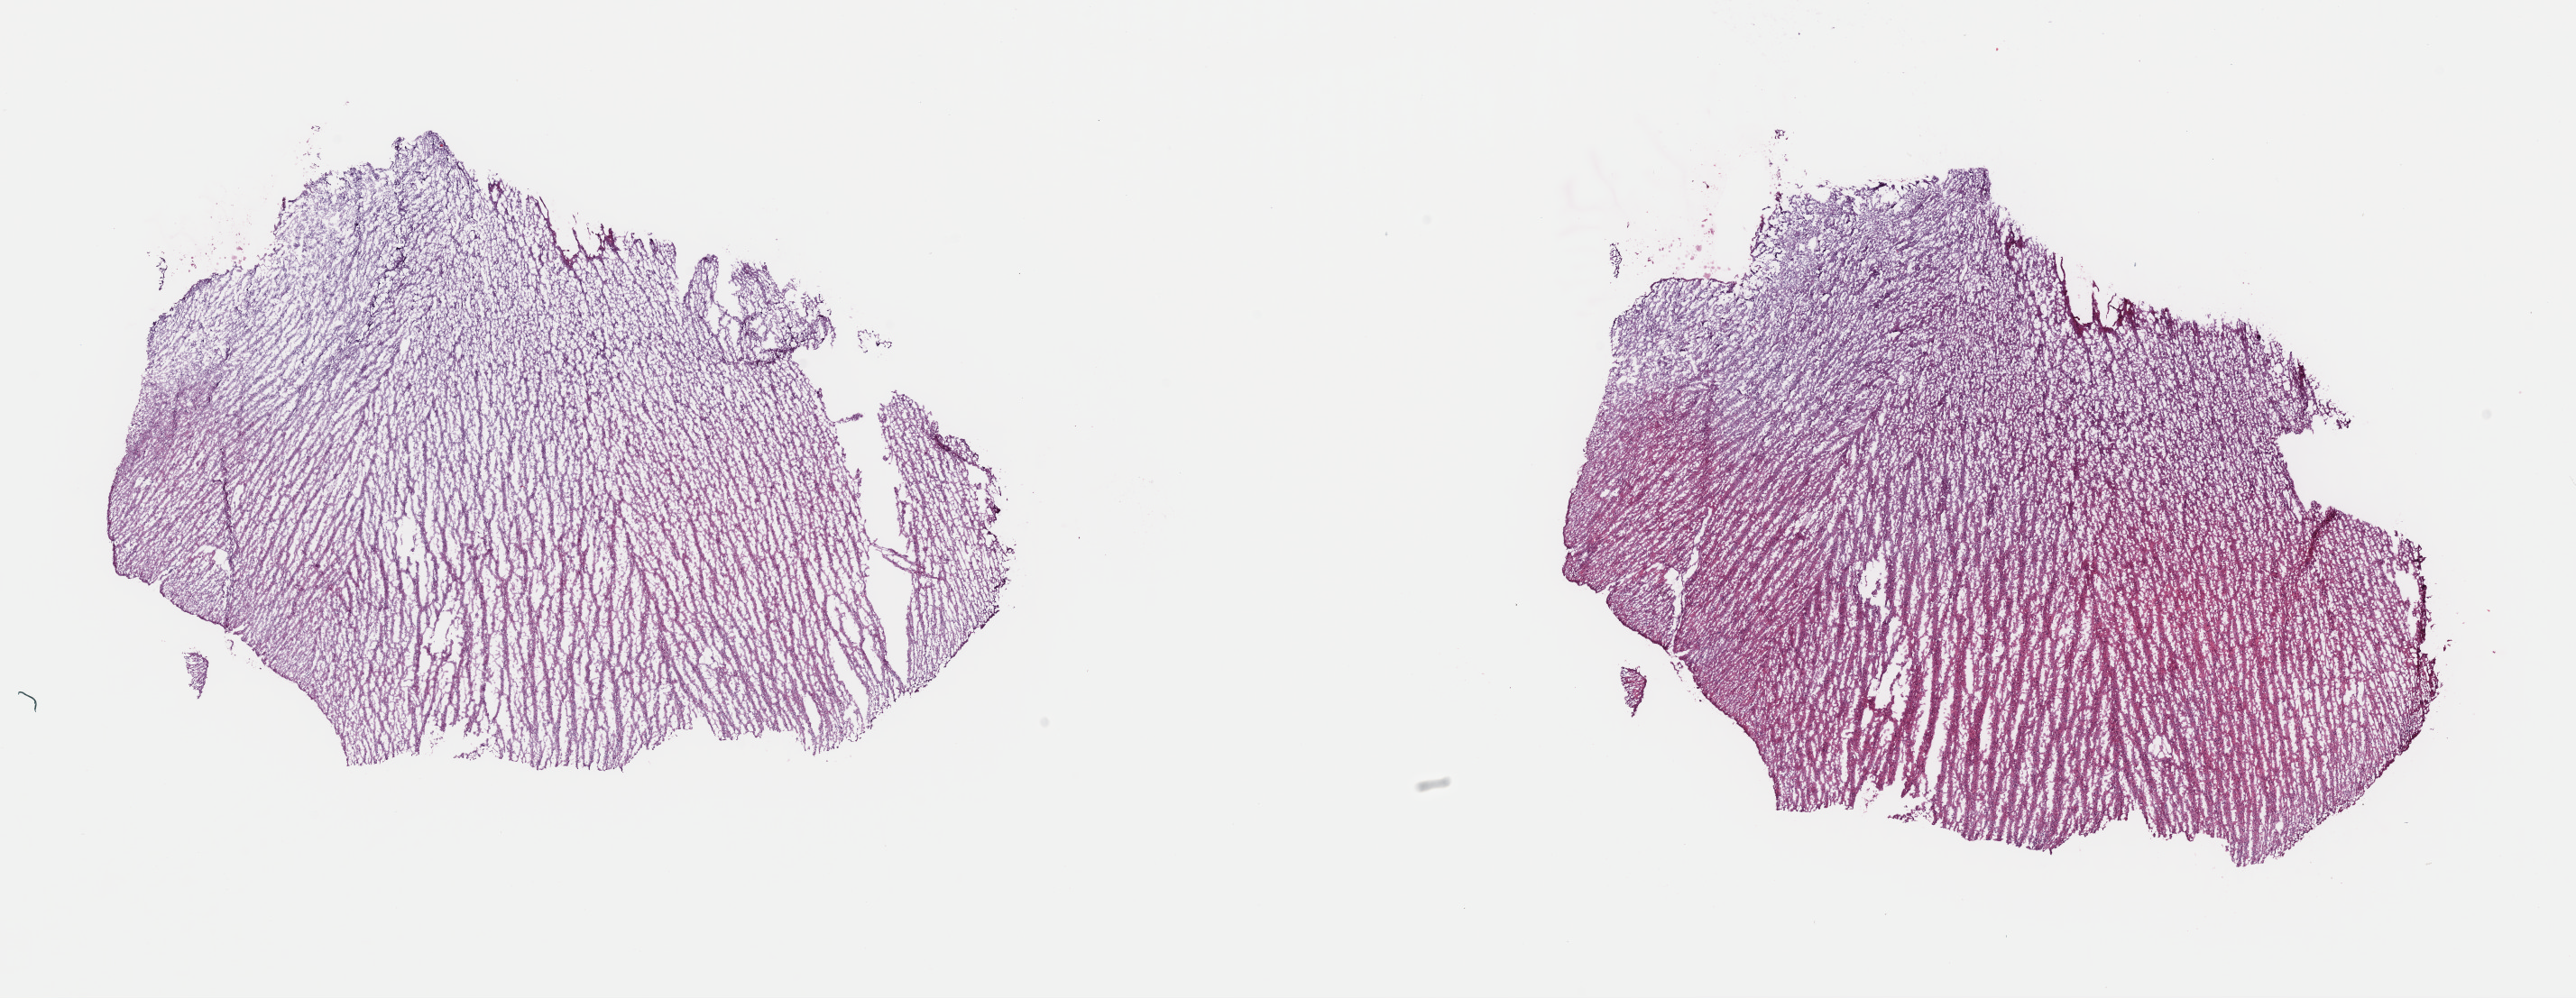
Digitized Hematoxylin and eosin (H&E) stained tissue section (whole slide), a low-resolution overview of the entire scanned area, about 22.6 x 8.7 mm; frozen section from the top of the tissue portion; brain, primary tumour sample. Female patient; age at initial diagnosis 55 years. Histologic grade: G2 (moderately differentiated). Slide review estimates, as recorded: tumour cells 40%, tumour nuclei 80%, normal cells 10%, stromal cells 50%, necrosis 0%. Inflammatory infiltration, as recorded: lymphocyte infiltration 0%, monocyte infiltration 0%, neutrophil infiltration 0%.
* pathologic diagnosis: Mixed glioma (cerebrum)